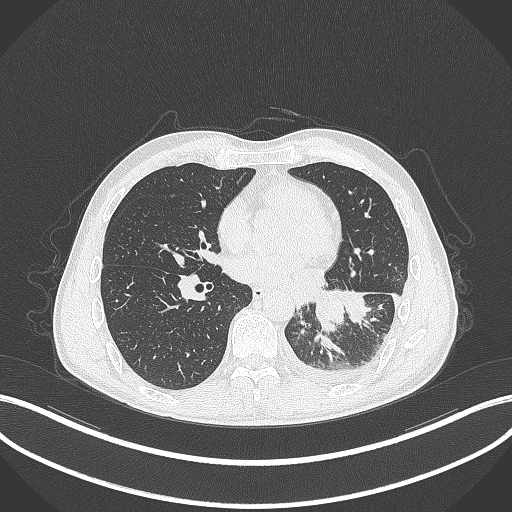
Chest CT, one axial slice. Slice 134 of 295 in the series (ordered by position). Reconstruction kernel B70f. Lung window (W 1500 / L -600 HU). 1 mm slice thickness. 512 × 512 image matrix. Male patient, age 47 years. From the clinical record (not read from this slice): clinical TNM (as recorded): T3 N1 M1c; histopathological grade: G3.
Outlined on this slice (rectangle marked by the reading radiologist):
- lung tumour (recorded histology: small cell carcinoma): box from (x=313, y=286) to (x=346, y=333) px